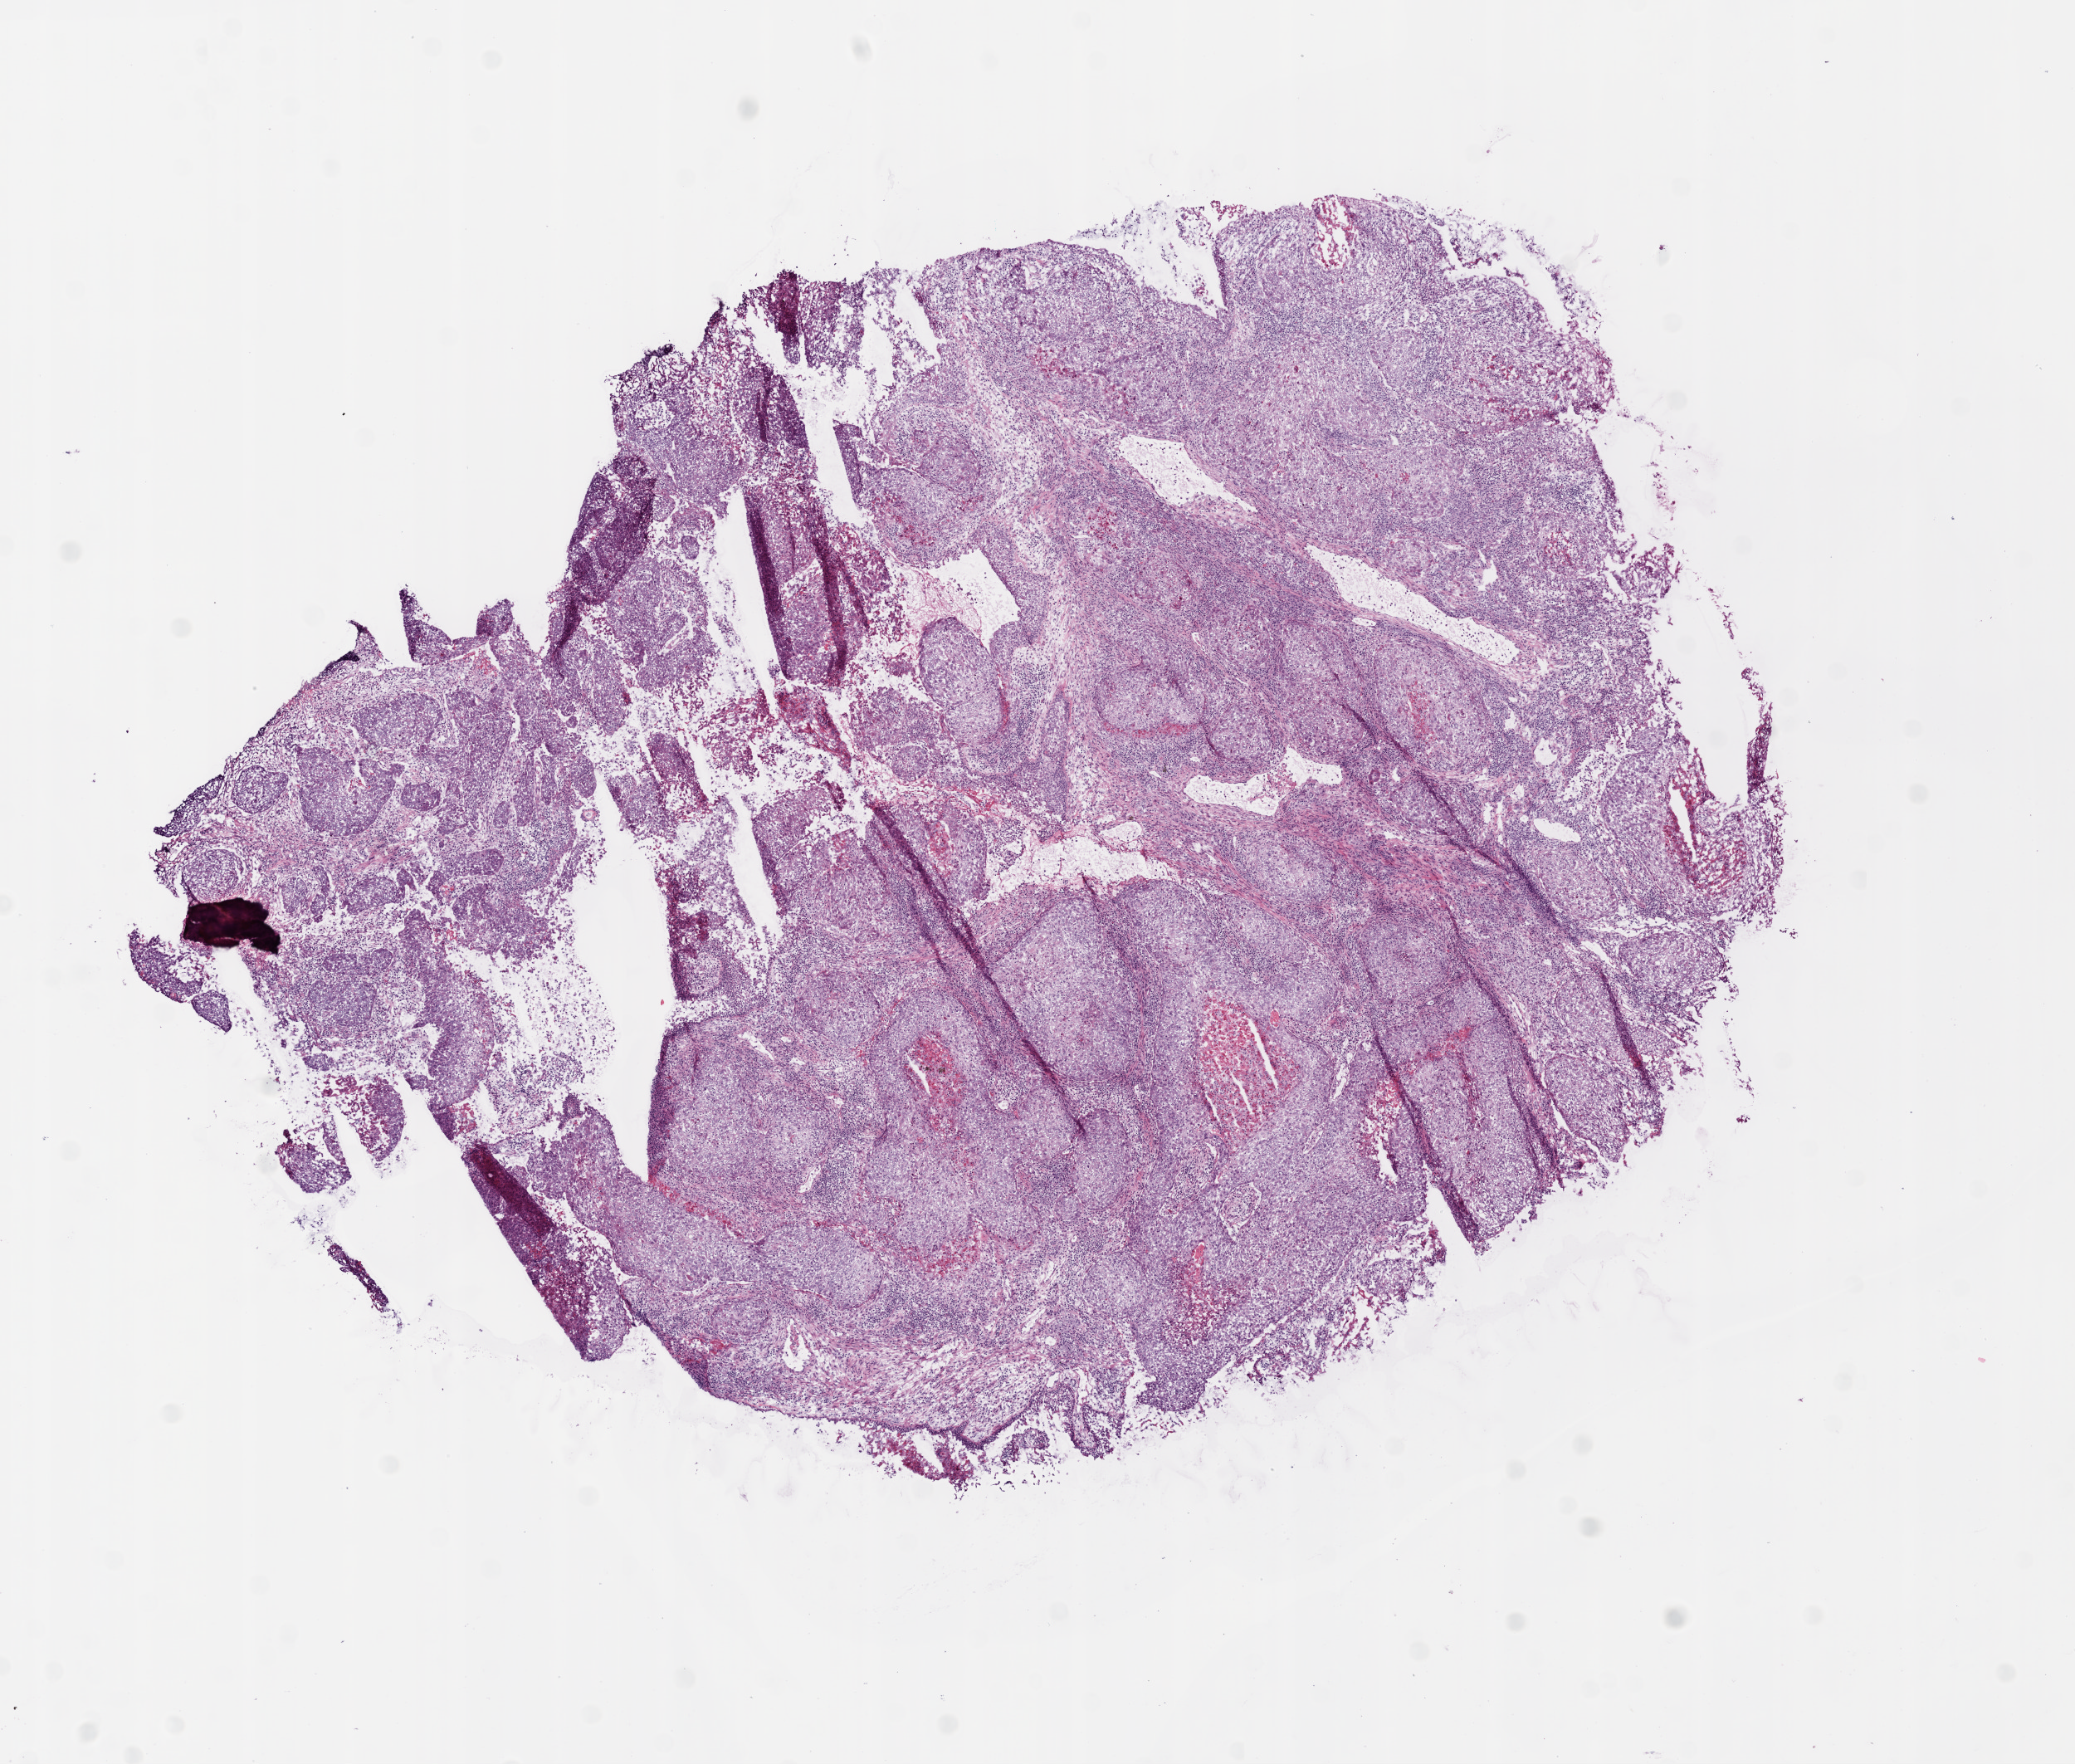
Hematoxylin and eosin (H&E) stained whole-slide image — shown as a low-resolution overview of the whole scanned area (about 10.0 x 8.5 mm, from a 20x scan); frozen section from the top of the tissue portion; lung, primary tumour sample. Male, age 51 years at initial diagnosis. Composition of this section per pathologist review: tumour cells 90%, tumour nuclei 60%, necrosis 10%. Inflammatory infiltration, as recorded: lymphocyte infiltration 30%, neutrophil infiltration 5%.
Laterality: left. AJCC pathologic stage: IIIA (7th edition). Pathologic diagnosis: Squamous cell carcinoma, NOS (upper lobe, lung).